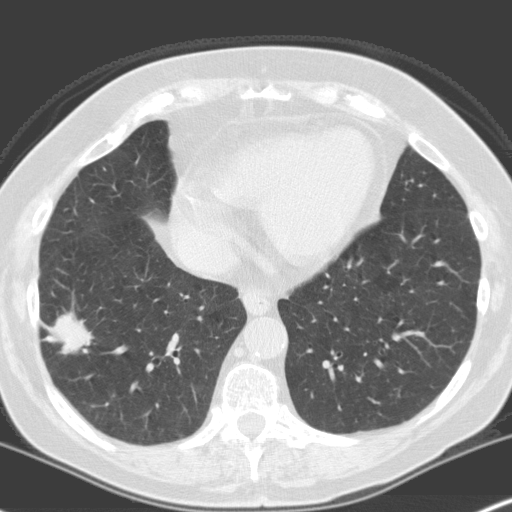
Low-dose screening chest CT, one axial slice. Slice 63 of 160 in the series (ordered by position). 120 kVp. Lung window (W 1500 / L -600 HU). 3.2 mm slice thickness. 512 × 512 image matrix.
Annotated regions visible in this slice (outlined manually by an expert reader):
- lesion 1 (tumor, lower lobe of right lung): bounding box <45,313,92,355> (left, top, right, bottom; pixels)